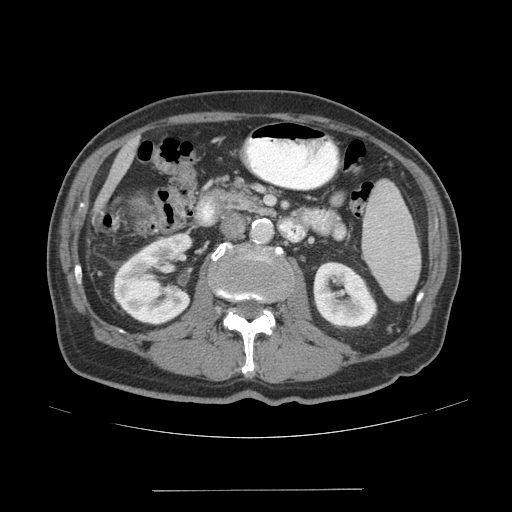
Contrast-enhanced abdominal CT (liver protocol), one axial slice. Slice 7 of 77 in the series (ordered by position). 140 kVp. Soft-tissue window (W 400 / L 40 HU). 2.5 mm slice thickness. 512 × 512 image matrix. Case-level facts recorded for this patient, not image findings: diagnosis: hepatocellular carcinoma (patient treated with transarterial chemoembolisation; whether this scan precedes or follows treatment is not stated here); TNM stage (as recorded): Stage-IVA; Child-Pugh class: A; tumour differentiation: well differentiated; tumour nodularity: uninodular.
Outlined on this slice (semi-automatic segmentation, software-assisted and operator-edited):
- liver parenchyma outside the tumour (the mass and vessels are separate outlines, so this box may not span the whole liver): box from (x=92, y=138) to (x=138, y=219) px